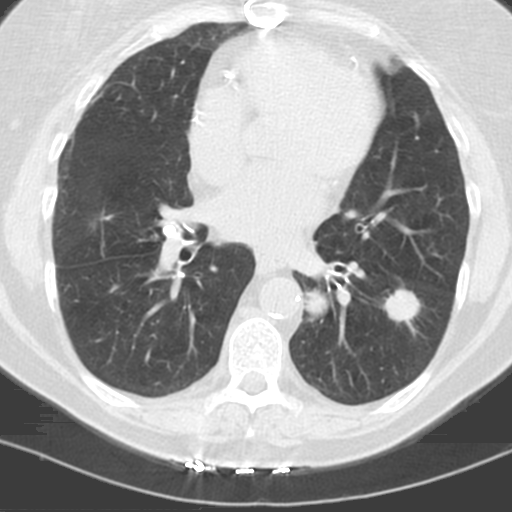
Chest CT (low-dose screening protocol), one axial image; baseline screening round; lung window (W 1500 / L -600 HU); 3.2 mm slice thickness; standard (soft-tissue) reconstruction kernel (C); slice 71 of 121 in the series. Female participant, aged 60 years at enrolment. Former smoker at enrolment.
2 lesions marked by an expert reader on this slice (largest first), bounding box <288,280,338,332> (left, top, right, bottom; pixels); <375,286,425,329>. The screening reader recorded 3 non-calcified nodules or masses ≥4 mm on this exam (left lower lobe, left lower lobe, right middle lobe); which of them these boxes mark is not recorded. Lung cancer was diagnosed 96 days after this screen: adenocarcinoma, NOS, left lower lobe, stage IV (AJCC 6th edition), 22 mm at pathology.